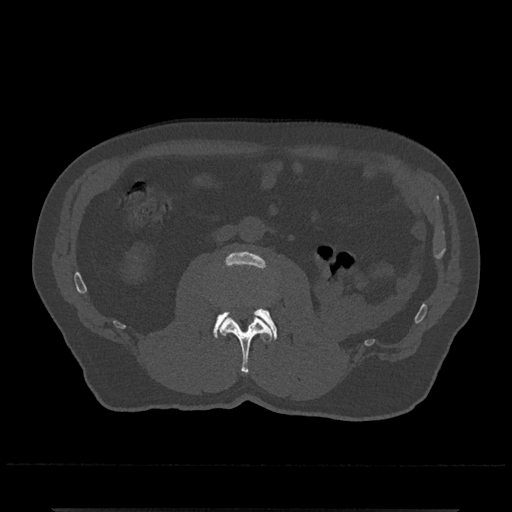
CT including the spine, one axial slice; position 263 of 797 along the scan axis; 120 kVp; bone window (W 1800 / L 400 HU); 512 × 512 image matrix, field of view 393 × 393 mm. Patient: male, 67 years. From the clinical record (not read from this slice): primary cancer: prostate.
Annotated regions visible in this slice (semi-automatic segmentation, software-assisted and operator-edited):
- L2 vertebra: box from (x=219, y=315) to (x=272, y=374) px
- L3 vertebra: (x=213, y=252)–(x=277, y=340)